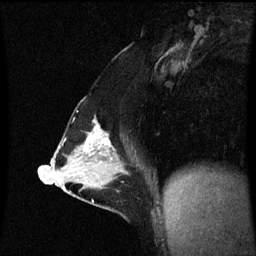
Breast MRI (dynamic contrast-enhanced), one sagittal slice; position 32 of 60 along the scan axis; dynamic contrast-enhanced series, image 2 of 3 at this slice position (ordered by acquisition); 1.5 T; TE 4.2 ms, TR 8.9 ms; 256 × 256 image matrix. Patient: female, 47 years. From the clinical record (not read from this slice): setting: breast cancer imaged before/during neoadjuvant chemotherapy; receptor status: HR-positive, HER2-negative.
Structures marked on this image (semi-automatically segmented with operator editing):
- analysis volume of interest (the breast-tissue region the enhancement analysis was run in; not a lesion): bounding box (x1, y1, x2, y2) in pixels: (53, 112, 131, 209)
- tumour enhancement mask (voxels above the 70 % enhancement threshold inside the analysis volume of interest): (85, 124, 112, 155)